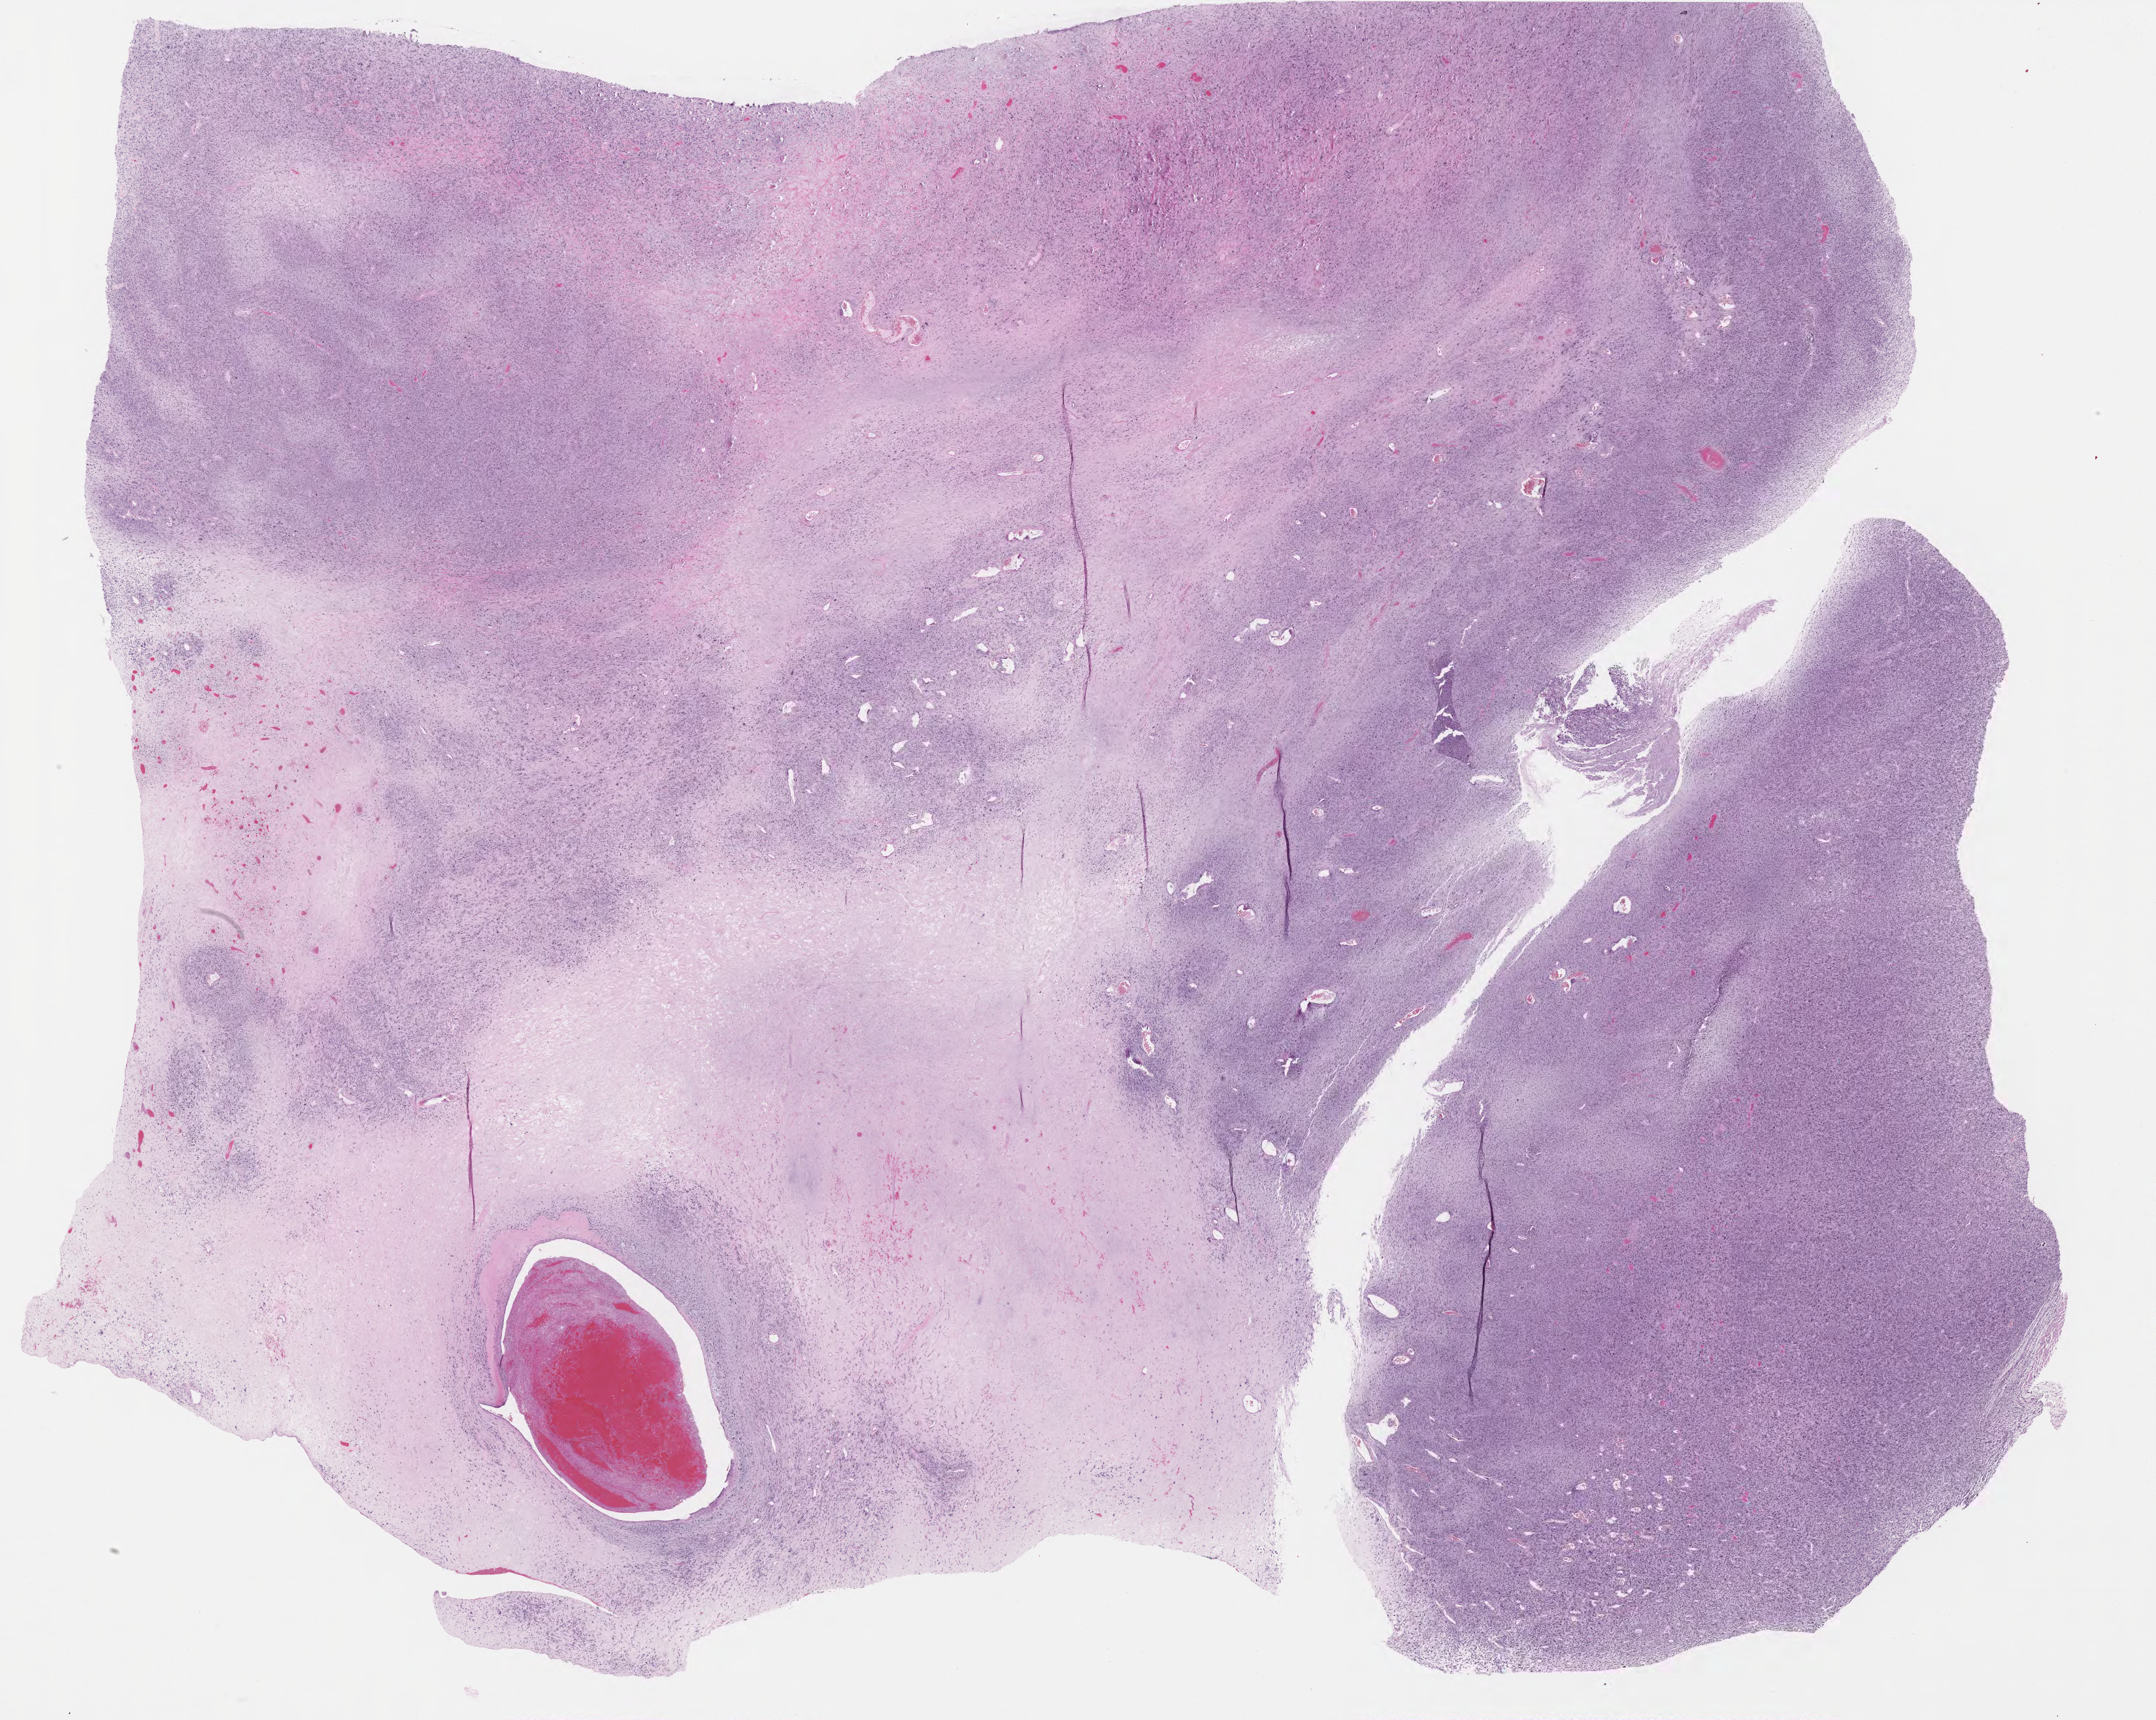
Digitized H&E-stained tissue section (whole slide), low-resolution overview of the scanned area, about 26.5 x 21.2 mm, FFPE section, primary tumour sample from the connective, subcutaneous and other soft tissues. Female patient; age at initial diagnosis 78 years.
Histologic diagnosis: Undifferentiated sarcoma (connective, subcutaneous and other soft tissues of lower limb and hip).